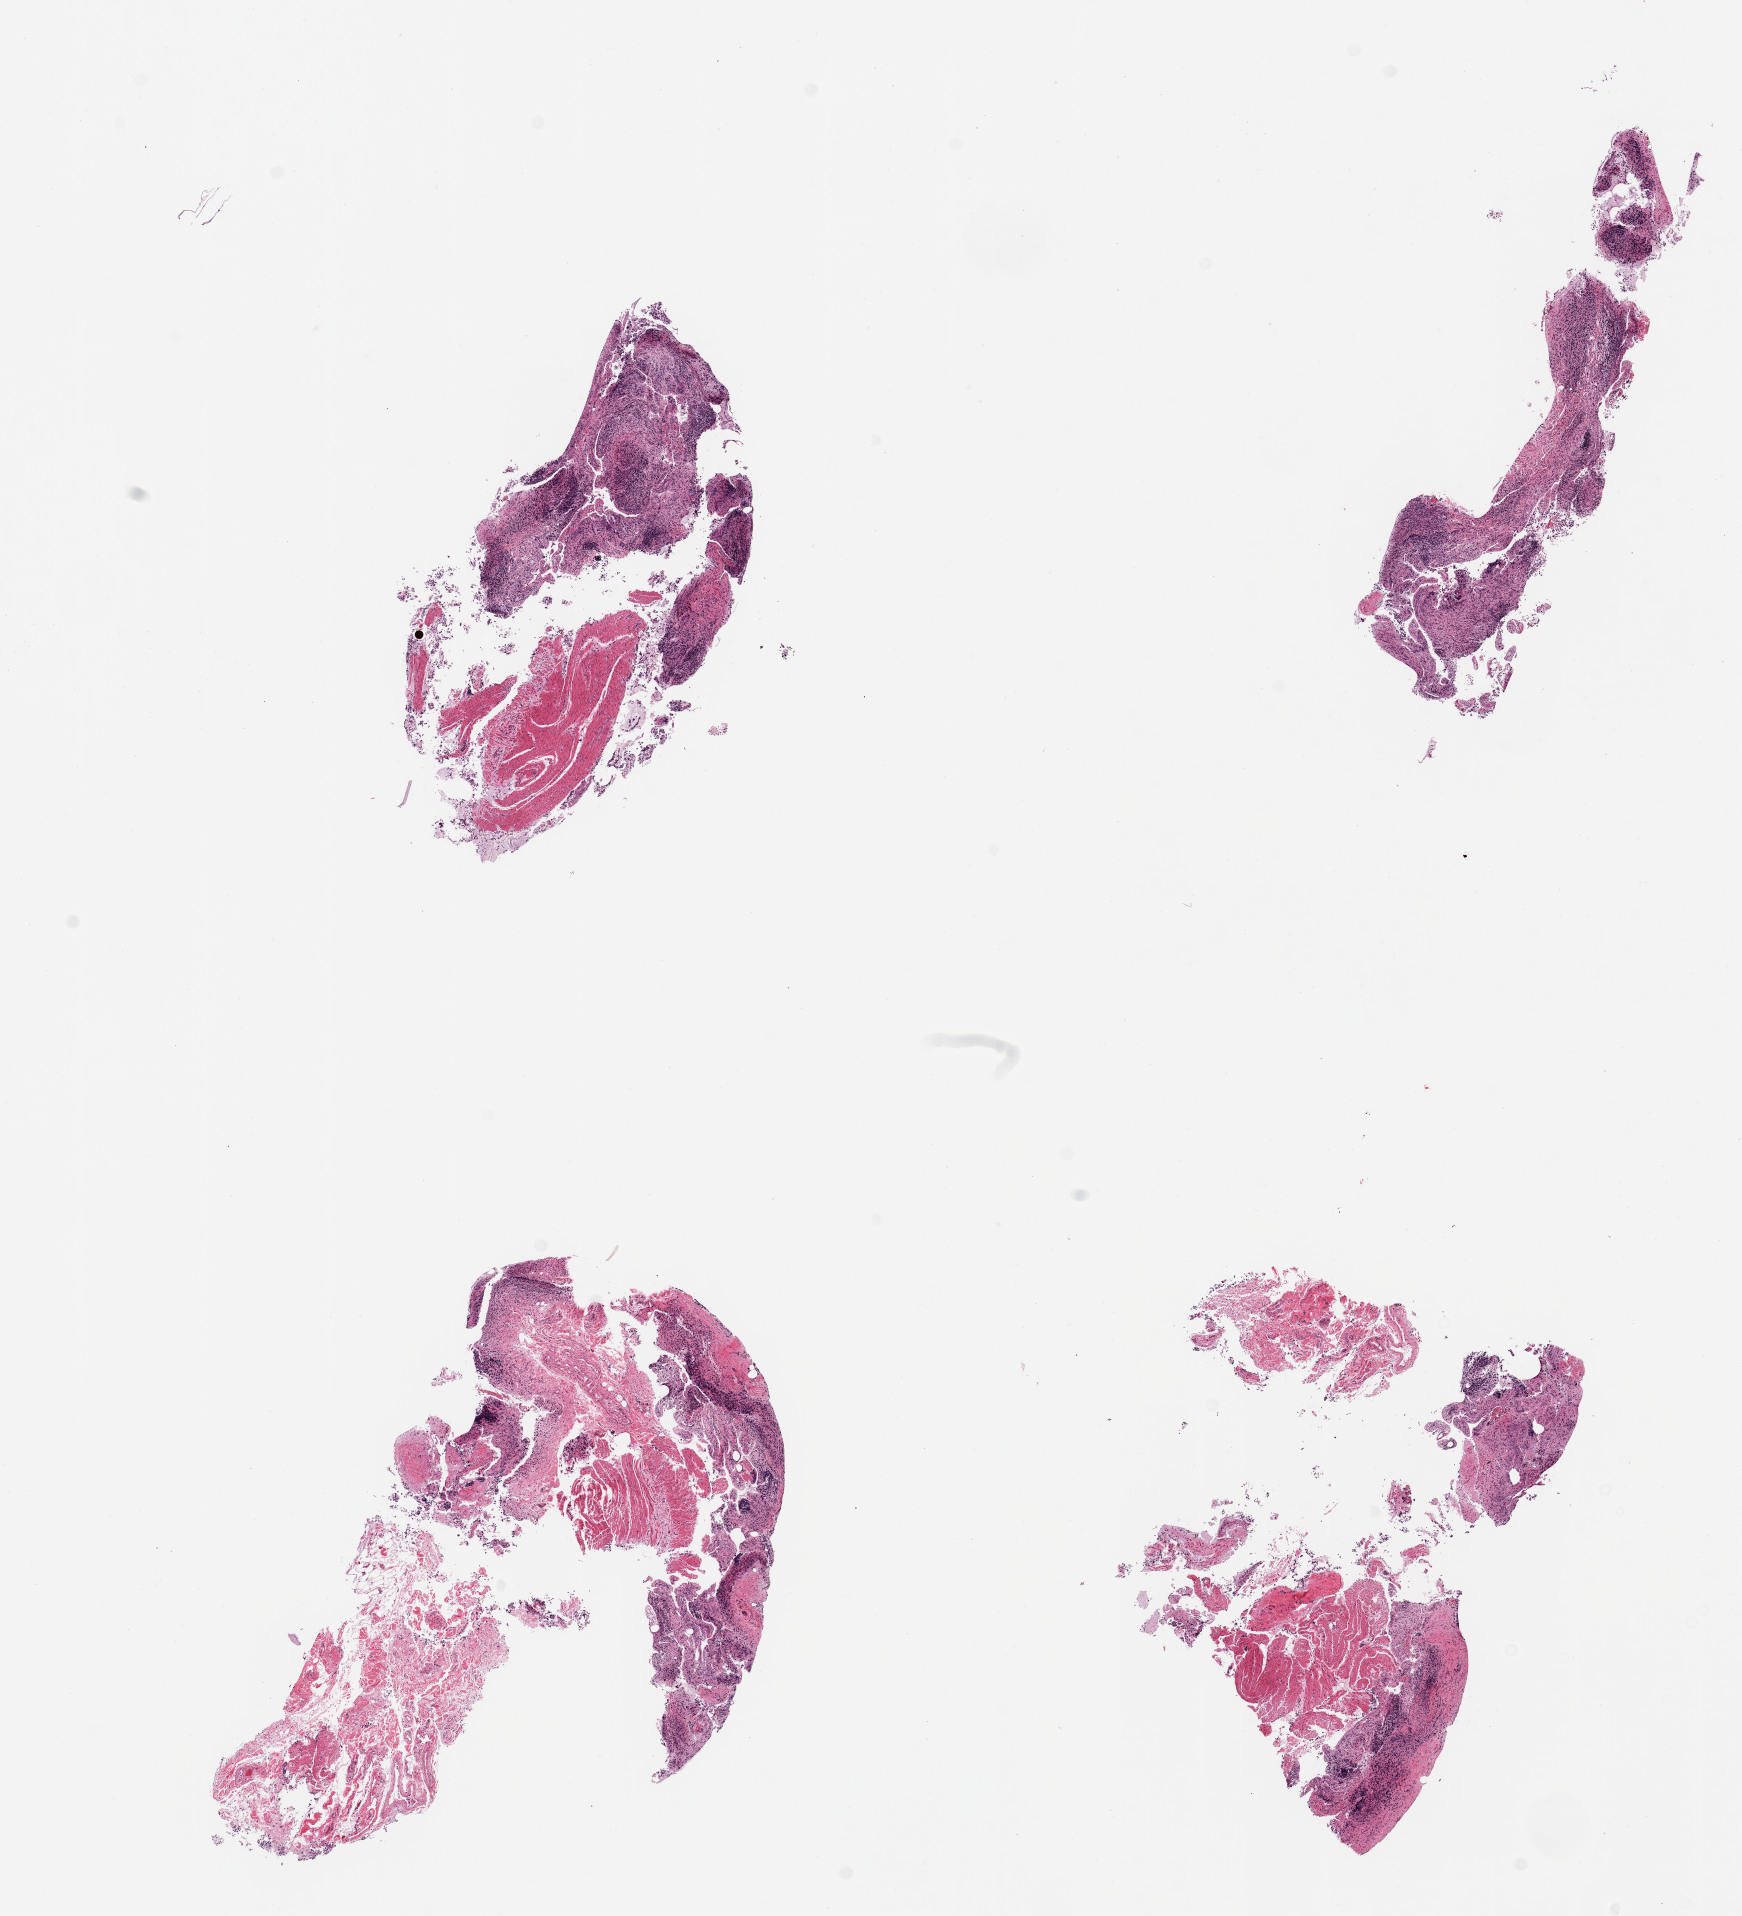
Haematoxylin and eosin whole-slide image — shown as a low-resolution overview of the whole scanned area (about 13.8 x 15.2 mm, slide scanned at 20x). PAXgene-fixed, paraffin-embedded tissue. Sampled site (target tissue): ileum. Tissue donor sample. Donor sex: male.
Review note (as recorded): 4 pieces, 10-20% lymphoid aggregates remain in sloughed mucosa.